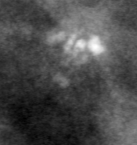
Region of interest cut from a scanned film mammogram (one marked finding); right breast; MLO view; BI-RADS breast density category 3 (scale 1–4).
- Marked abnormality: calcifications, morphology dystrophic, distribution clustered; BI-RADS assessment category 3; subtlety rating 4 on a 1 (subtle) to 5 (obvious) scale; pathology (as recorded): benign.